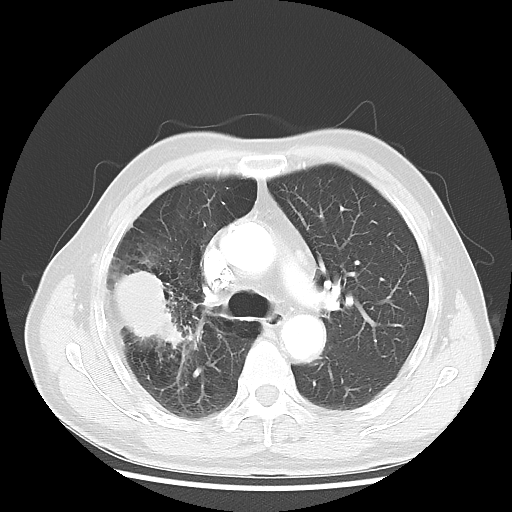
Chest CT, one axial slice. Position 32 of 50 along the scan axis. Lung window (W 1500 / L -600 HU). 5 mm slice thickness. 512 × 512 image matrix, field of view 360 × 360 mm. Male patient, age 69 years. Case-level facts recorded for this patient, not image findings: clinical TNM (as recorded): T3 N0 M0; histopathological grade: G3.
Annotated regions visible in this slice (rectangle marked by the reading radiologist):
- lung tumour (recorded histology: adenocarcinoma): bounding box <109,267,187,348> (left, top, right, bottom; pixels)